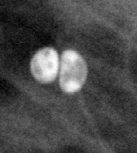
Cropped region of a digitized screen-film mammogram centred on a radiologist-marked abnormality, left breast, MLO view, BI-RADS breast density category 3 (scale 1–4).
Finding: calcifications, morphology lucent center; BI-RADS assessment category 2; subtlety rating 3 on a 1 (subtle) to 5 (obvious) scale; benign; no additional work-up was recommended (benign without callback).